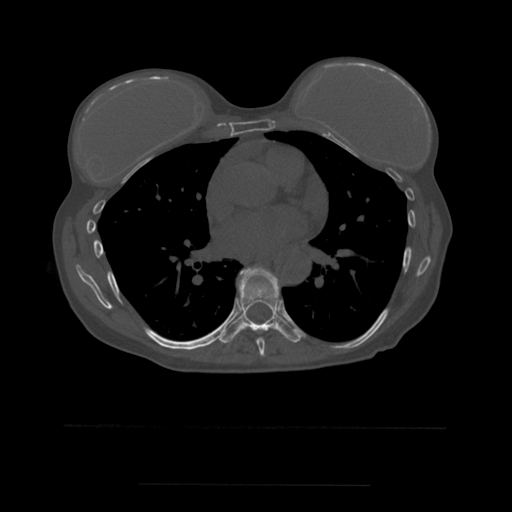
CT including the spine, one axial slice. Bone window (W 1800 / L 400 HU). 1.25 mm slice thickness. 512 × 512 image matrix, field of view 350 × 350 mm. Patient age 58 years. From the clinical record (not read from this slice): primary cancer: lung.
Structures marked on this image (semi-automatic segmentation, software-assisted and operator-edited):
- T7 vertebra: box from (x=239, y=270) to (x=279, y=357) px
- T8 vertebra: (x=220, y=267)–(x=302, y=343)